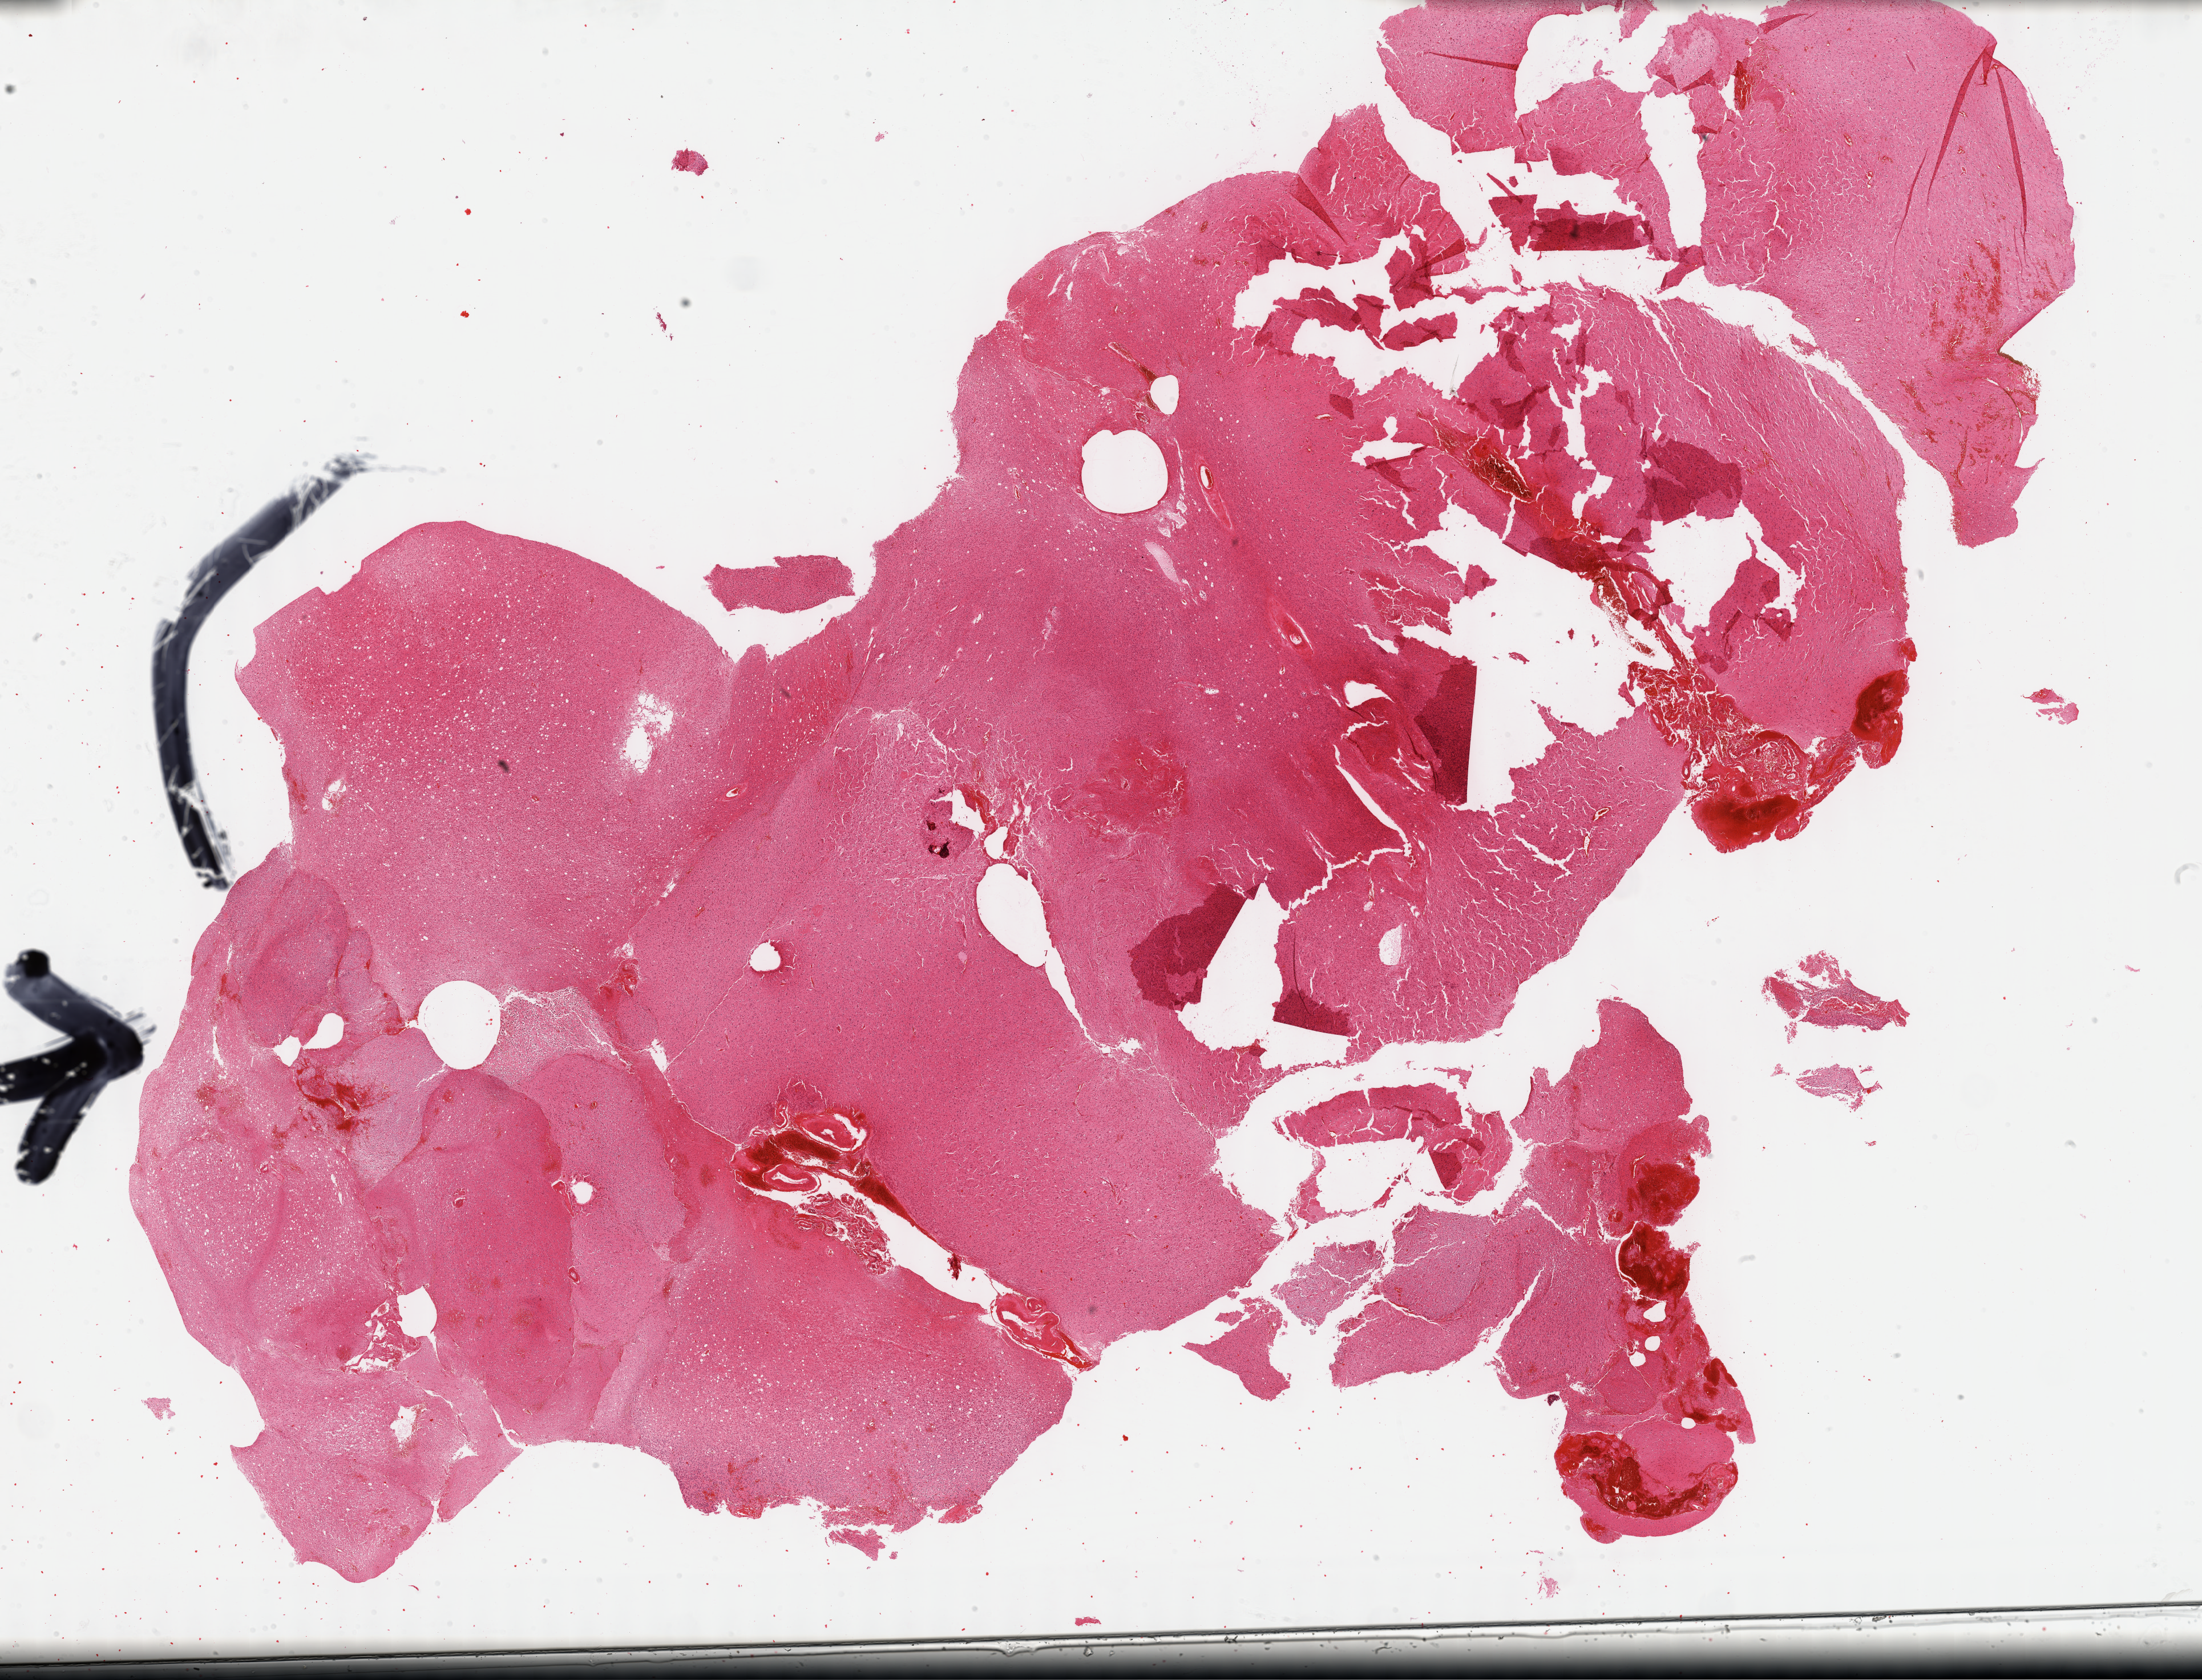
Whole-slide histology image, H&E-stained — low-resolution overview of the scanned area, about 31.2 x 23.8 mm (slide scanned at 40x); formalin-fixed paraffin-embedded (FFPE) diagnostic section; primary tumour sample from the brain. Female patient; age at initial diagnosis 35 years. Histologic grade: G2 (moderately differentiated).
• histologic diagnosis: Mixed glioma
• laterality: left